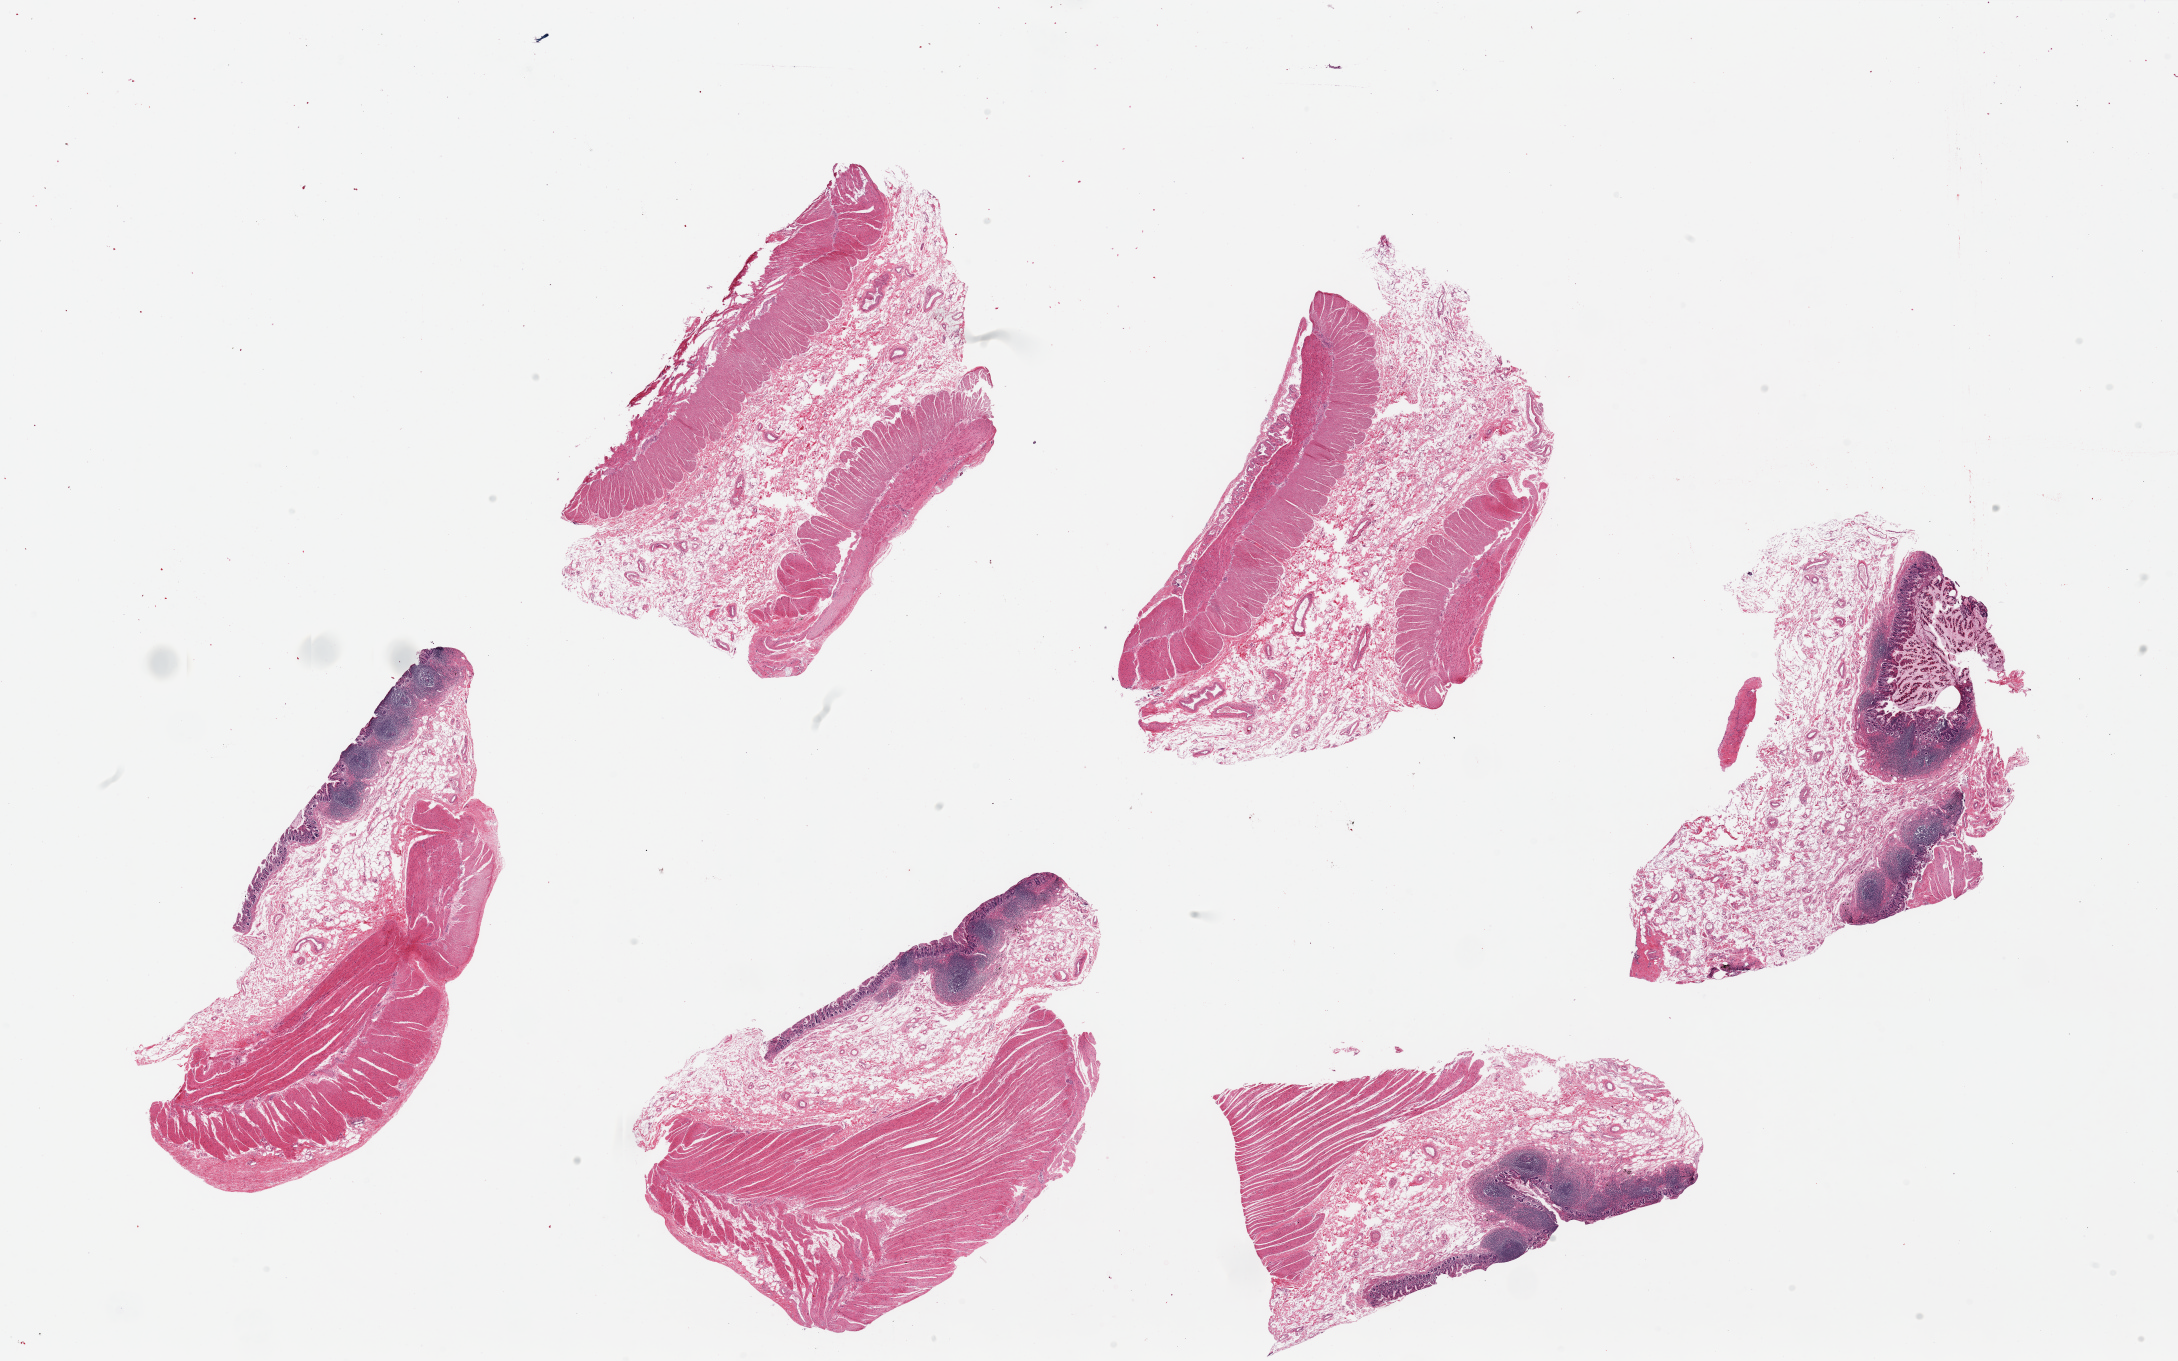
Digitized H&E-stained section, shown as a low-resolution overview of the whole scanned area (about 34.5 x 21.5 mm, acquisition: 20x scan); PAXgene-fixed, paraffin-embedded tissue; section of ileum (target tissue); donor tissue sample. Male donor.
Reviewer comment on this tissue sample: 6 pieces, up to 9x4mm; 4 of 6 have targeted 6 pieces, up to mucosa/submucosa with lymphoid tissue, but 5 of 6 have (unwanted) muscularis propria.